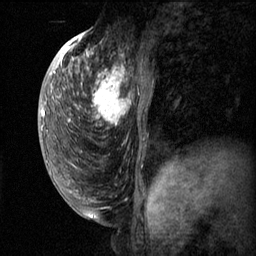
Breast MRI (dynamic contrast-enhanced), one sagittal slice; slice 30 of 60 in the series (ordered by position); dynamic contrast-enhanced series, image 2 of 3 at this slice position (ordered by acquisition); 1.5 T; TE 4.2 ms, TR 11.1 ms; 2 mm slice thickness; 256 × 256 image matrix, field of view 180 × 180 mm. Female patient, age 50 years.
Structures marked on this image (semi-automatic segmentation, software-assisted and operator-edited):
- analysis volume of interest (the breast-tissue region the enhancement analysis was run in; not a lesion): bounding box [x1, y1, x2, y2] px = [82, 56, 153, 143]
- tumour enhancement mask (voxels above the 70 % enhancement threshold inside the analysis volume of interest): [87, 56, 131, 127]